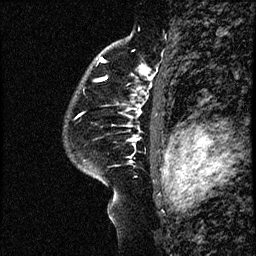
Breast MRI (dynamic contrast-enhanced), one sagittal slice; position 45 of 60 along the scan axis; dynamic contrast-enhanced study with each time point stored as its own series, time point 2 of 4 at this slice position (early post-contrast, ordered by acquisition time); 1.5 T; TE 4.2 ms, TR 17.6 ms; 2 mm slice thickness; 256 × 256 image matrix, field of view 200 × 200 mm. Patient: female, 43 years. From the clinical record (not read from this slice): setting: breast cancer imaged before/during neoadjuvant chemotherapy.
Annotated regions visible in this slice (semi-automatically segmented with operator editing):
- analysis volume of interest (the breast-tissue region the enhancement analysis was run in; not a lesion): bounding box [x1, y1, x2, y2] px = [67, 97, 169, 191]
- tumour enhancement mask (voxels above the 100 % enhancement threshold inside the analysis volume of interest): [133, 138, 136, 140]